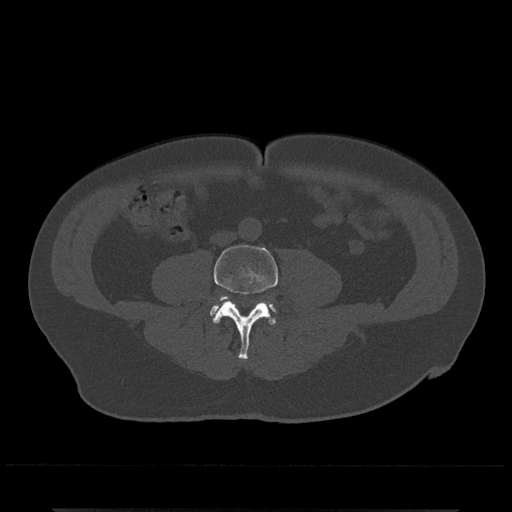
CT including the spine, one axial slice. Reconstruction kernel Br40s/3. Bone window (W 1800 / L 400 HU). 0.5 mm slice thickness. 512 × 512 image matrix, field of view 393 × 393 mm. Male patient, age 67 years. Case-level facts recorded for this patient, not image findings: primary cancer: prostate.
Structures marked on this image (semi-automatic segmentation, software-assisted and operator-edited):
- L4 vertebra: box from (x=214, y=244) to (x=278, y=360) px
- L5 vertebra: (x=210, y=297)–(x=275, y=318)